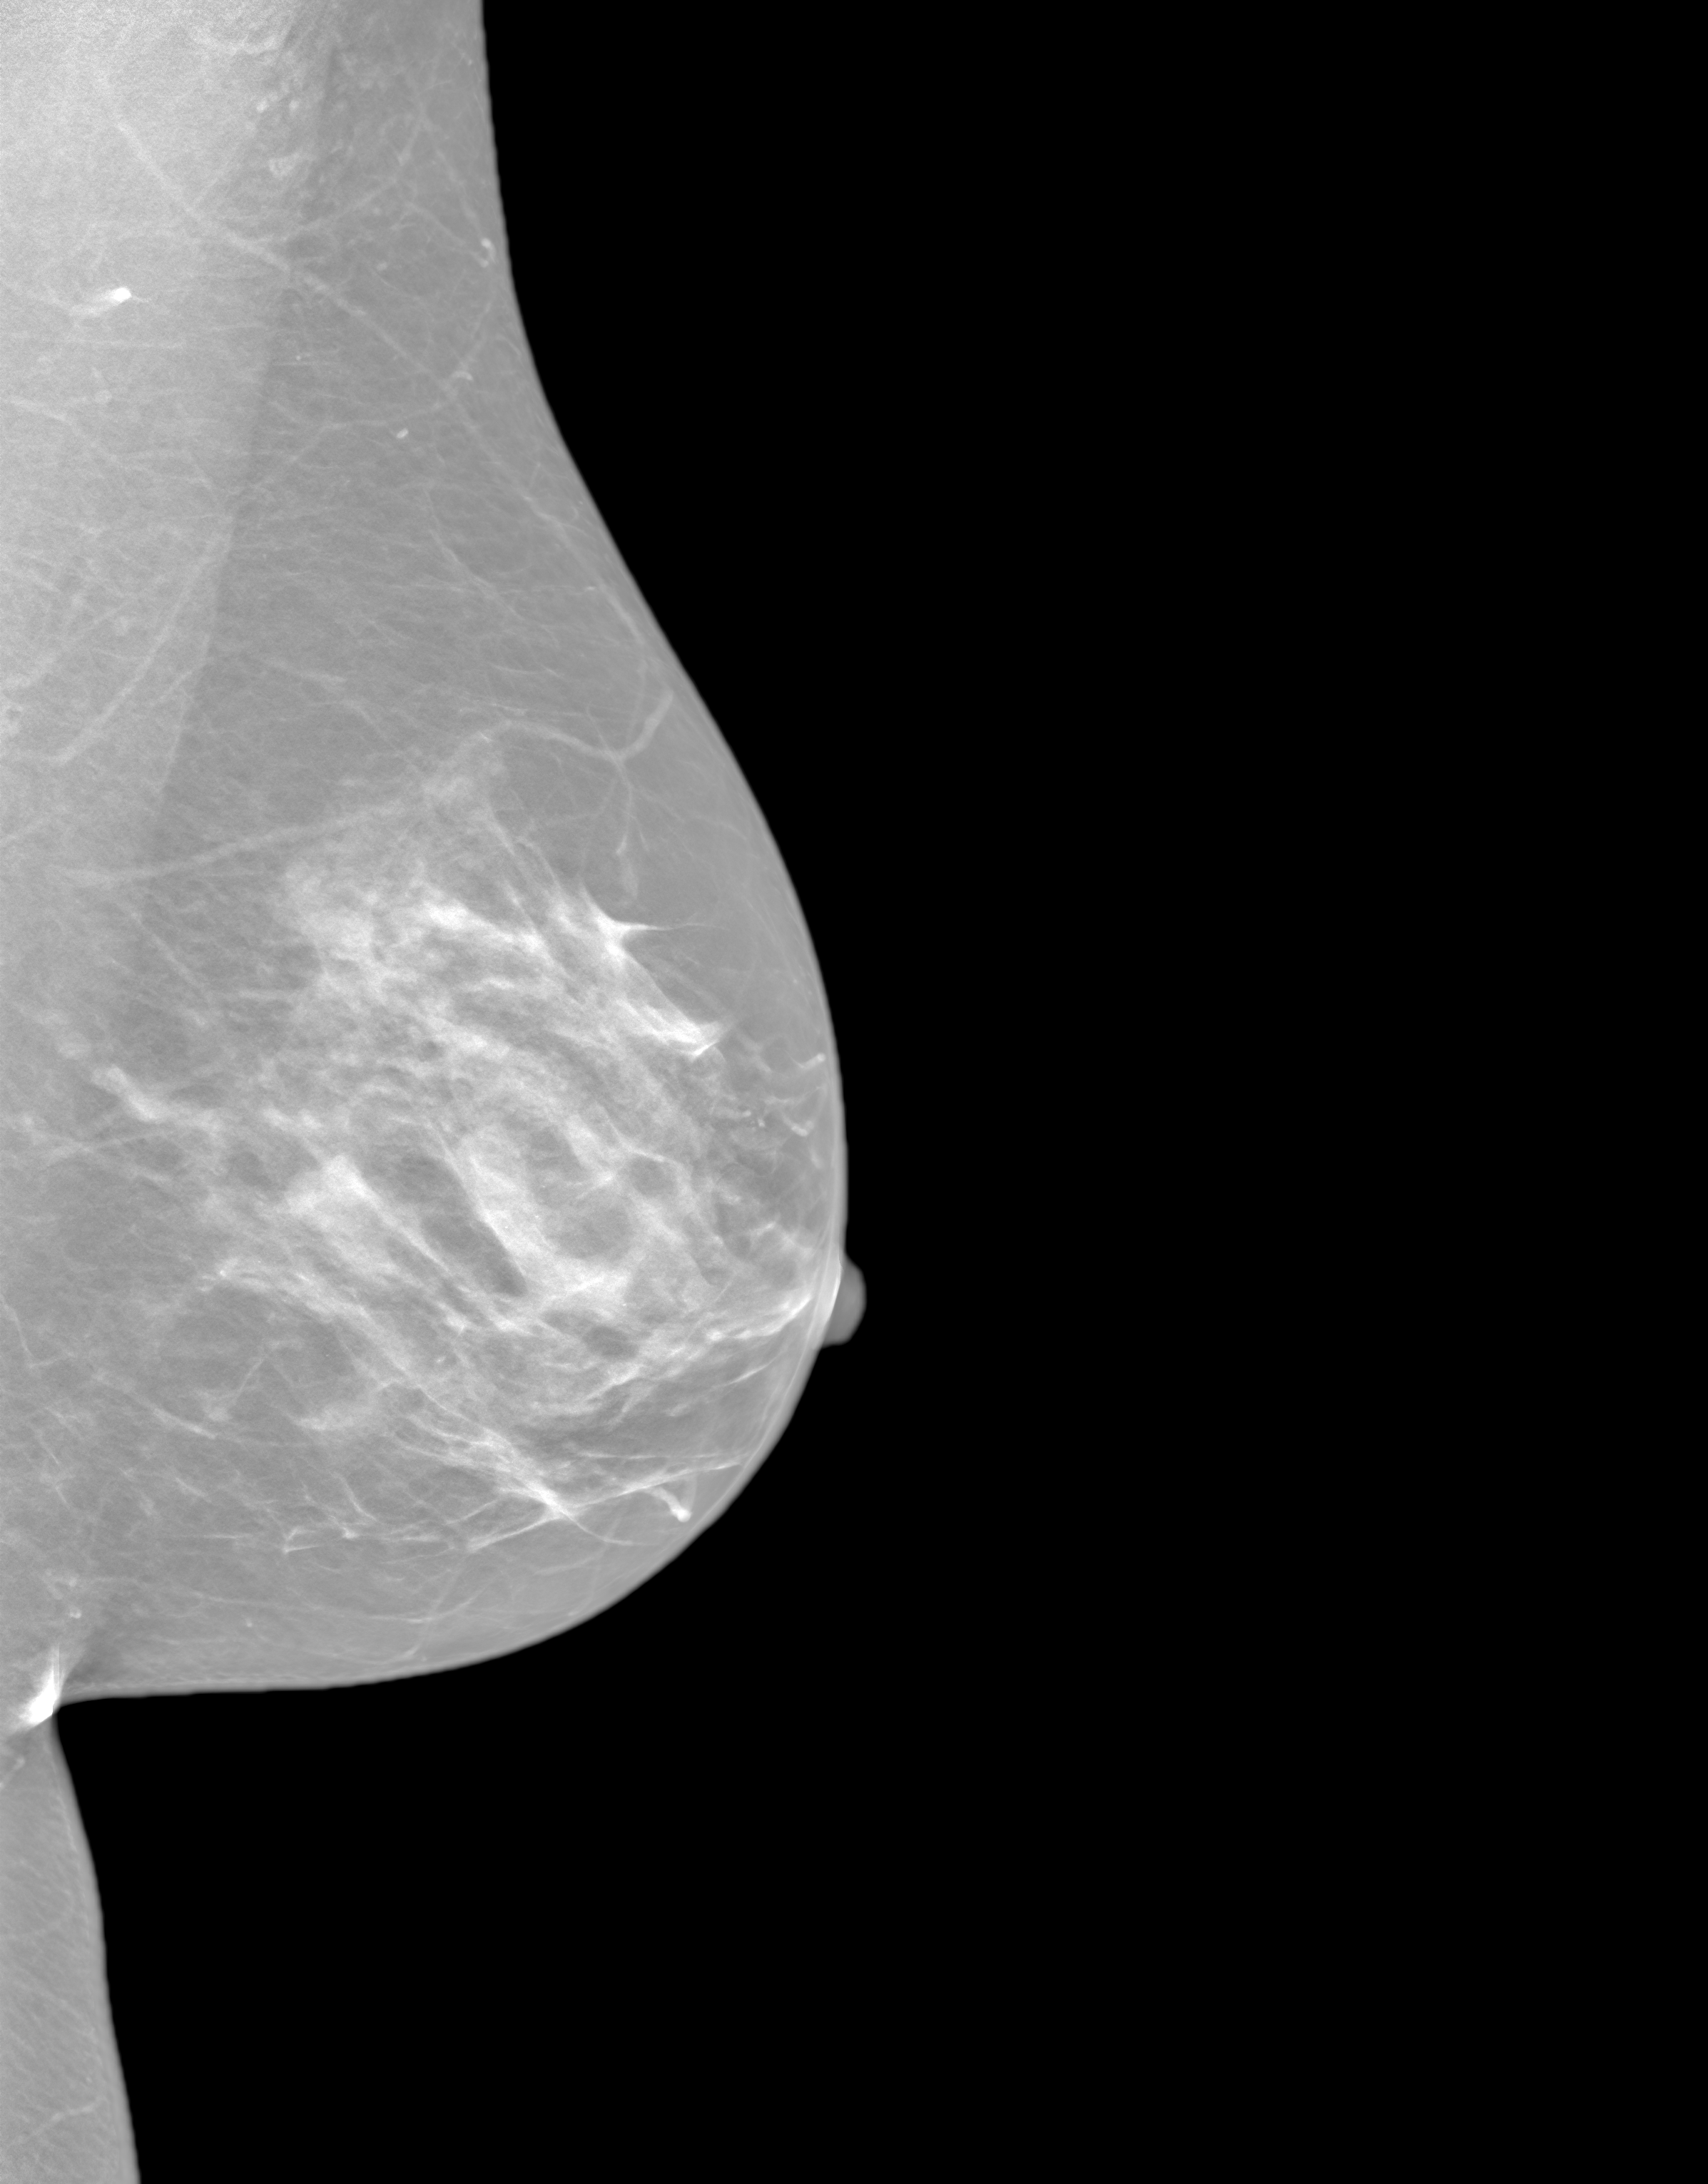
Screening examination. Patient: female, 46 years.
Image type: synthesized 2-D view from tomosynthesis. Breast: left. Projection: MLO view.